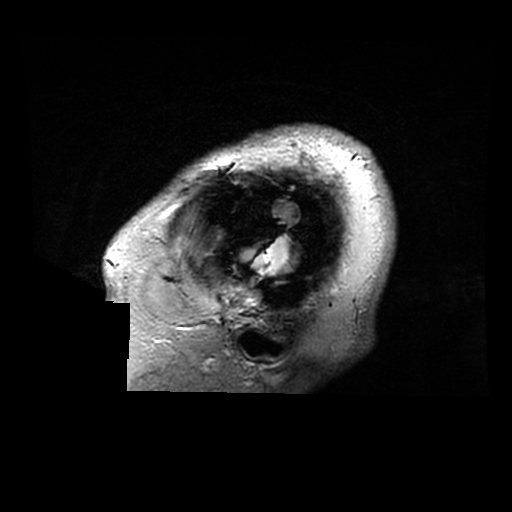
Brain MRI from a brain-tumour surgery series, one sagittal slice. Slice 264 of 320 in the series (ordered by position). 0.6 mm slice thickness. 512 × 512 image matrix. Case-level facts recorded for this patient, not image findings: histopathology: Astrocytoma; WHO grade: 2; IDH mutation: yes.
Annotated regions visible in this slice (manually delineated by an expert):
- tumour: bounding box [x1, y1, x2, y2] px = [245, 236, 297, 275]